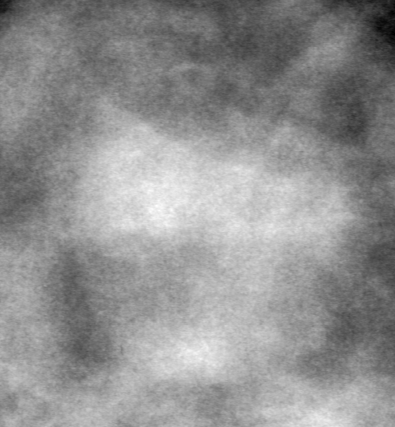
Cropped region of a digitized screen-film mammogram centred on a radiologist-marked abnormality; left breast; MLO view; BI-RADS breast density category 3 (scale 1–4).
- Marked abnormality: mass, shape round, margins circumscribed; BI-RADS assessment category 4; subtlety rating 4 on a 1 (subtle) to 5 (obvious) scale; pathology (as recorded): benign.